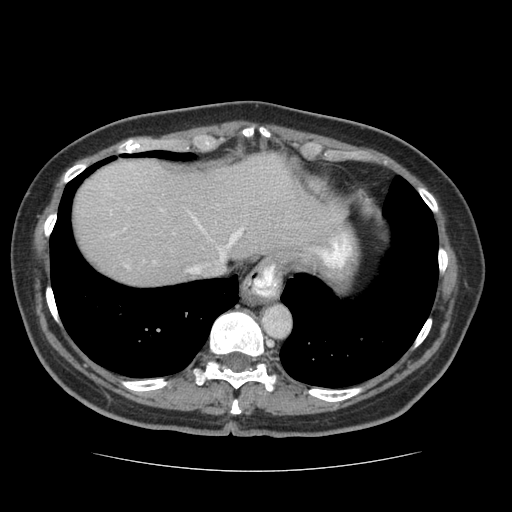
Contrast-enhanced abdominal CT (liver protocol), one axial slice. Slice 61 of 75 in the series (ordered by position). 140 kVp. Soft-tissue window (W 400 / L 40 HU). 2.5 mm slice thickness. 512 × 512 image matrix, field of view 360 × 360 mm. Case-level facts recorded for this patient, not image findings: diagnosis: hepatocellular carcinoma (patient treated with transarterial chemoembolisation; whether this scan precedes or follows treatment is not stated here); TNM stage (as recorded): Stage-I; Child-Pugh class: A; tumour differentiation: moderately differentiated; tumour nodularity: uninodular.
Structures marked on this image (semi-automatic segmentation, software-assisted and operator-edited):
- abdominal aorta: bounding box (x1, y1, x2, y2) in pixels: (263, 305, 290, 336)
- liver parenchyma outside the tumour (the mass and vessels are separate outlines, so this box may not span the whole liver): (72, 154, 350, 284)
- liver vessels: (111, 164, 349, 268)